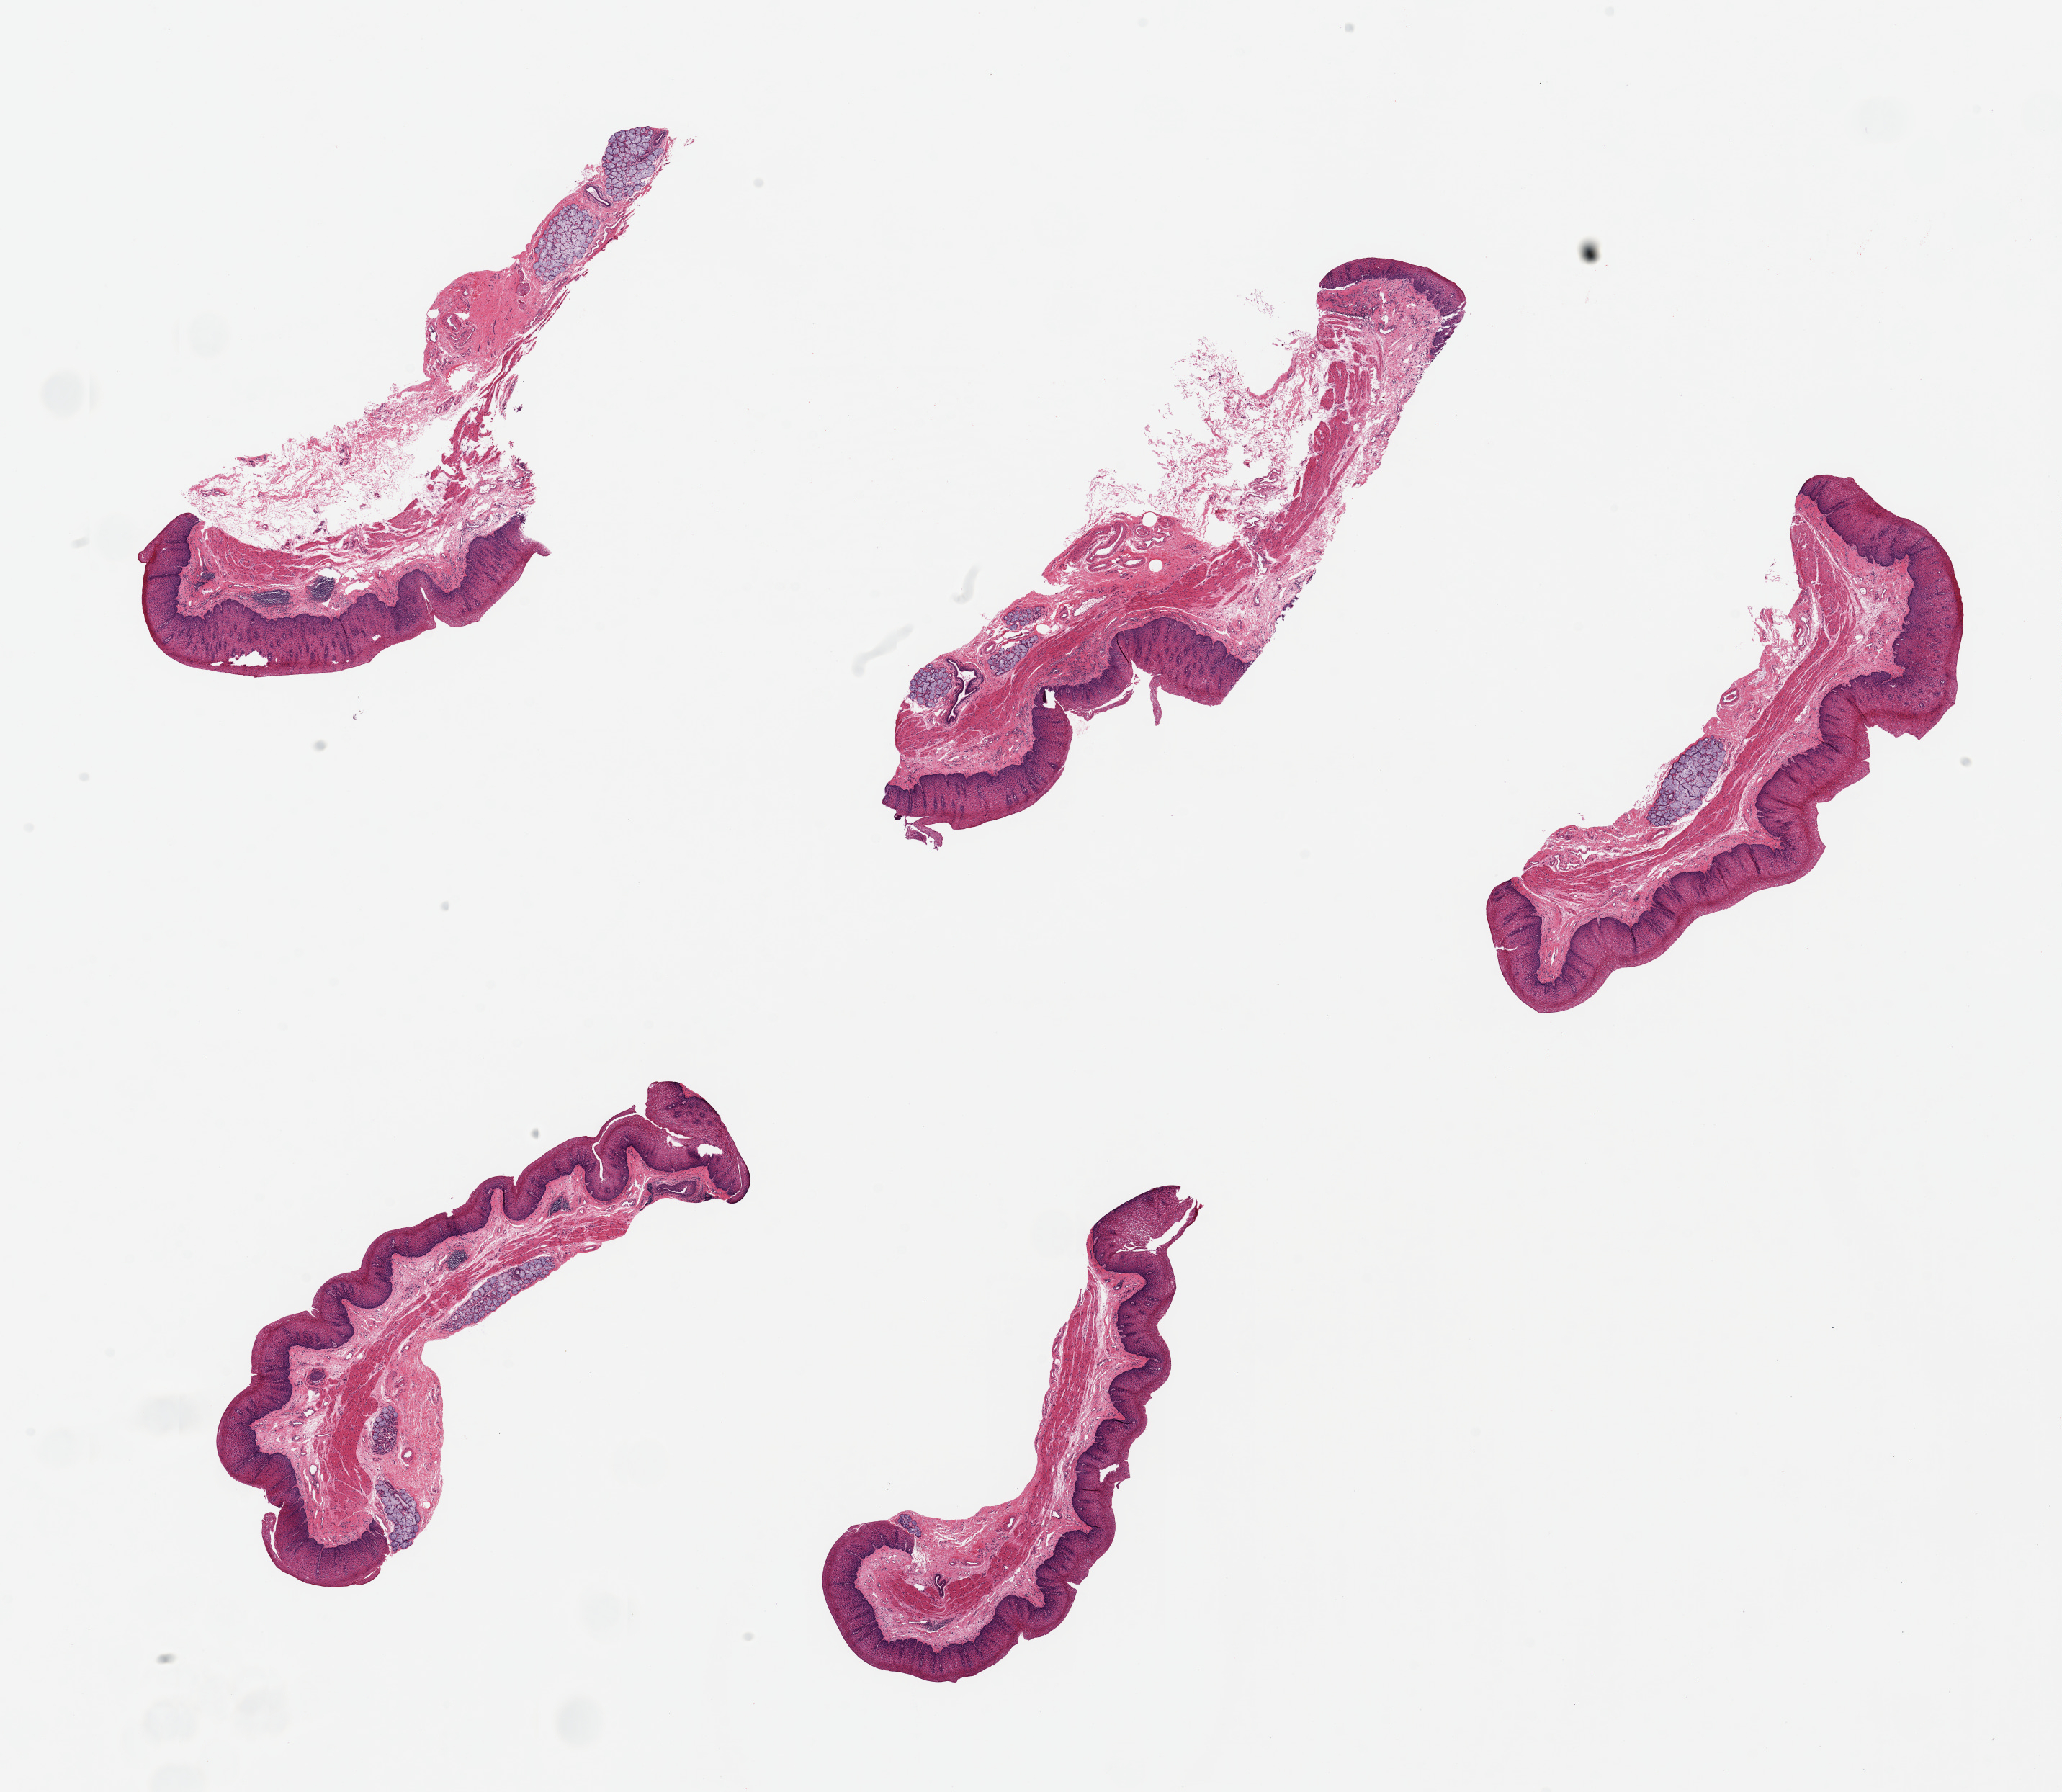
Hematoxylin and eosin (H&E) whole-slide image, brightfield, low-resolution overview of the scanned area, about 22.6 x 19.7 mm (acquisition: 20x scan); PAXgene-fixed paraffin-embedded (PFPE) section; sampled site (target tissue): gastroesophageal junction; tissue donor sample. Male donor.
Review note (as recorded): 5 pieces ~7x2mm, ~50% squamous mucosa, minimal muscle.